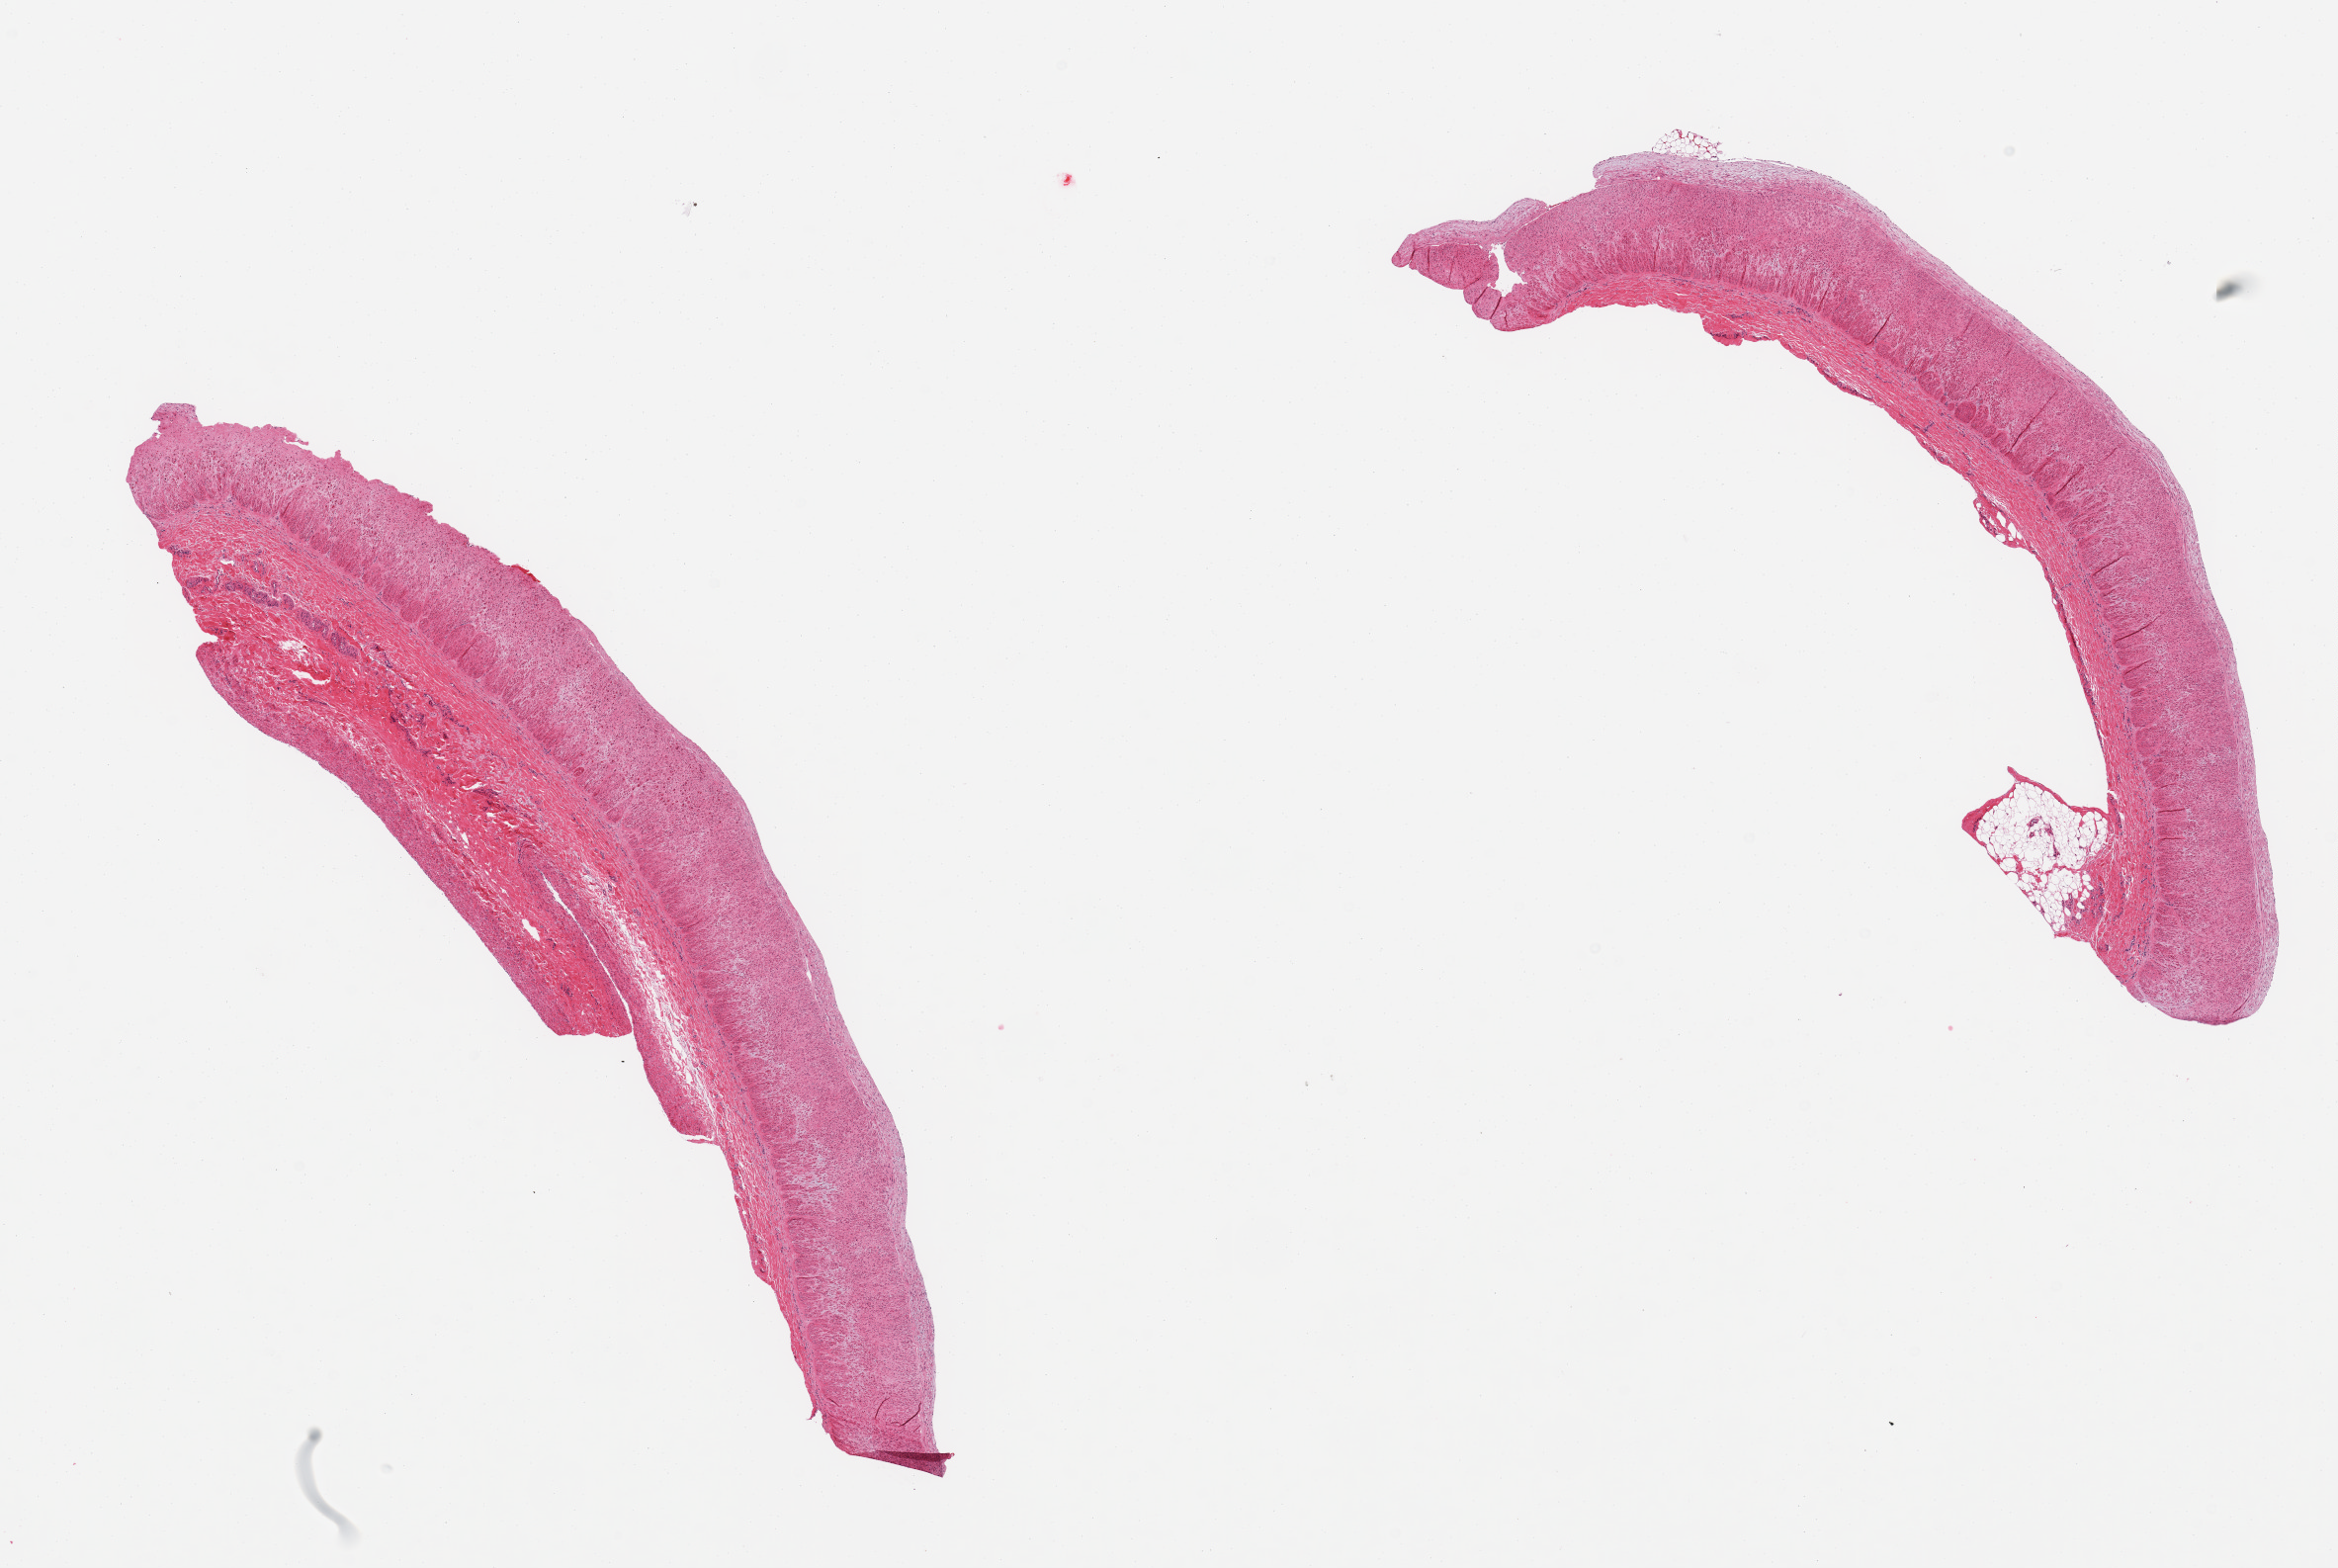
Whole-slide image, H&E stain, low-resolution overview of the scanned area, about 18.7 x 12.5 mm (from a 20x scan), PAXgene-fixed, paraffin-embedded tissue, section of tibial artery (target tissue), tissue donor sample. Donor: male.
Reviewer comment on this tissue sample: 2 pieces, no significant atherosis or adherent fat, partial edge of fibrous tissue up to ~1.5mm (sections are longitudinal, not cross sections).